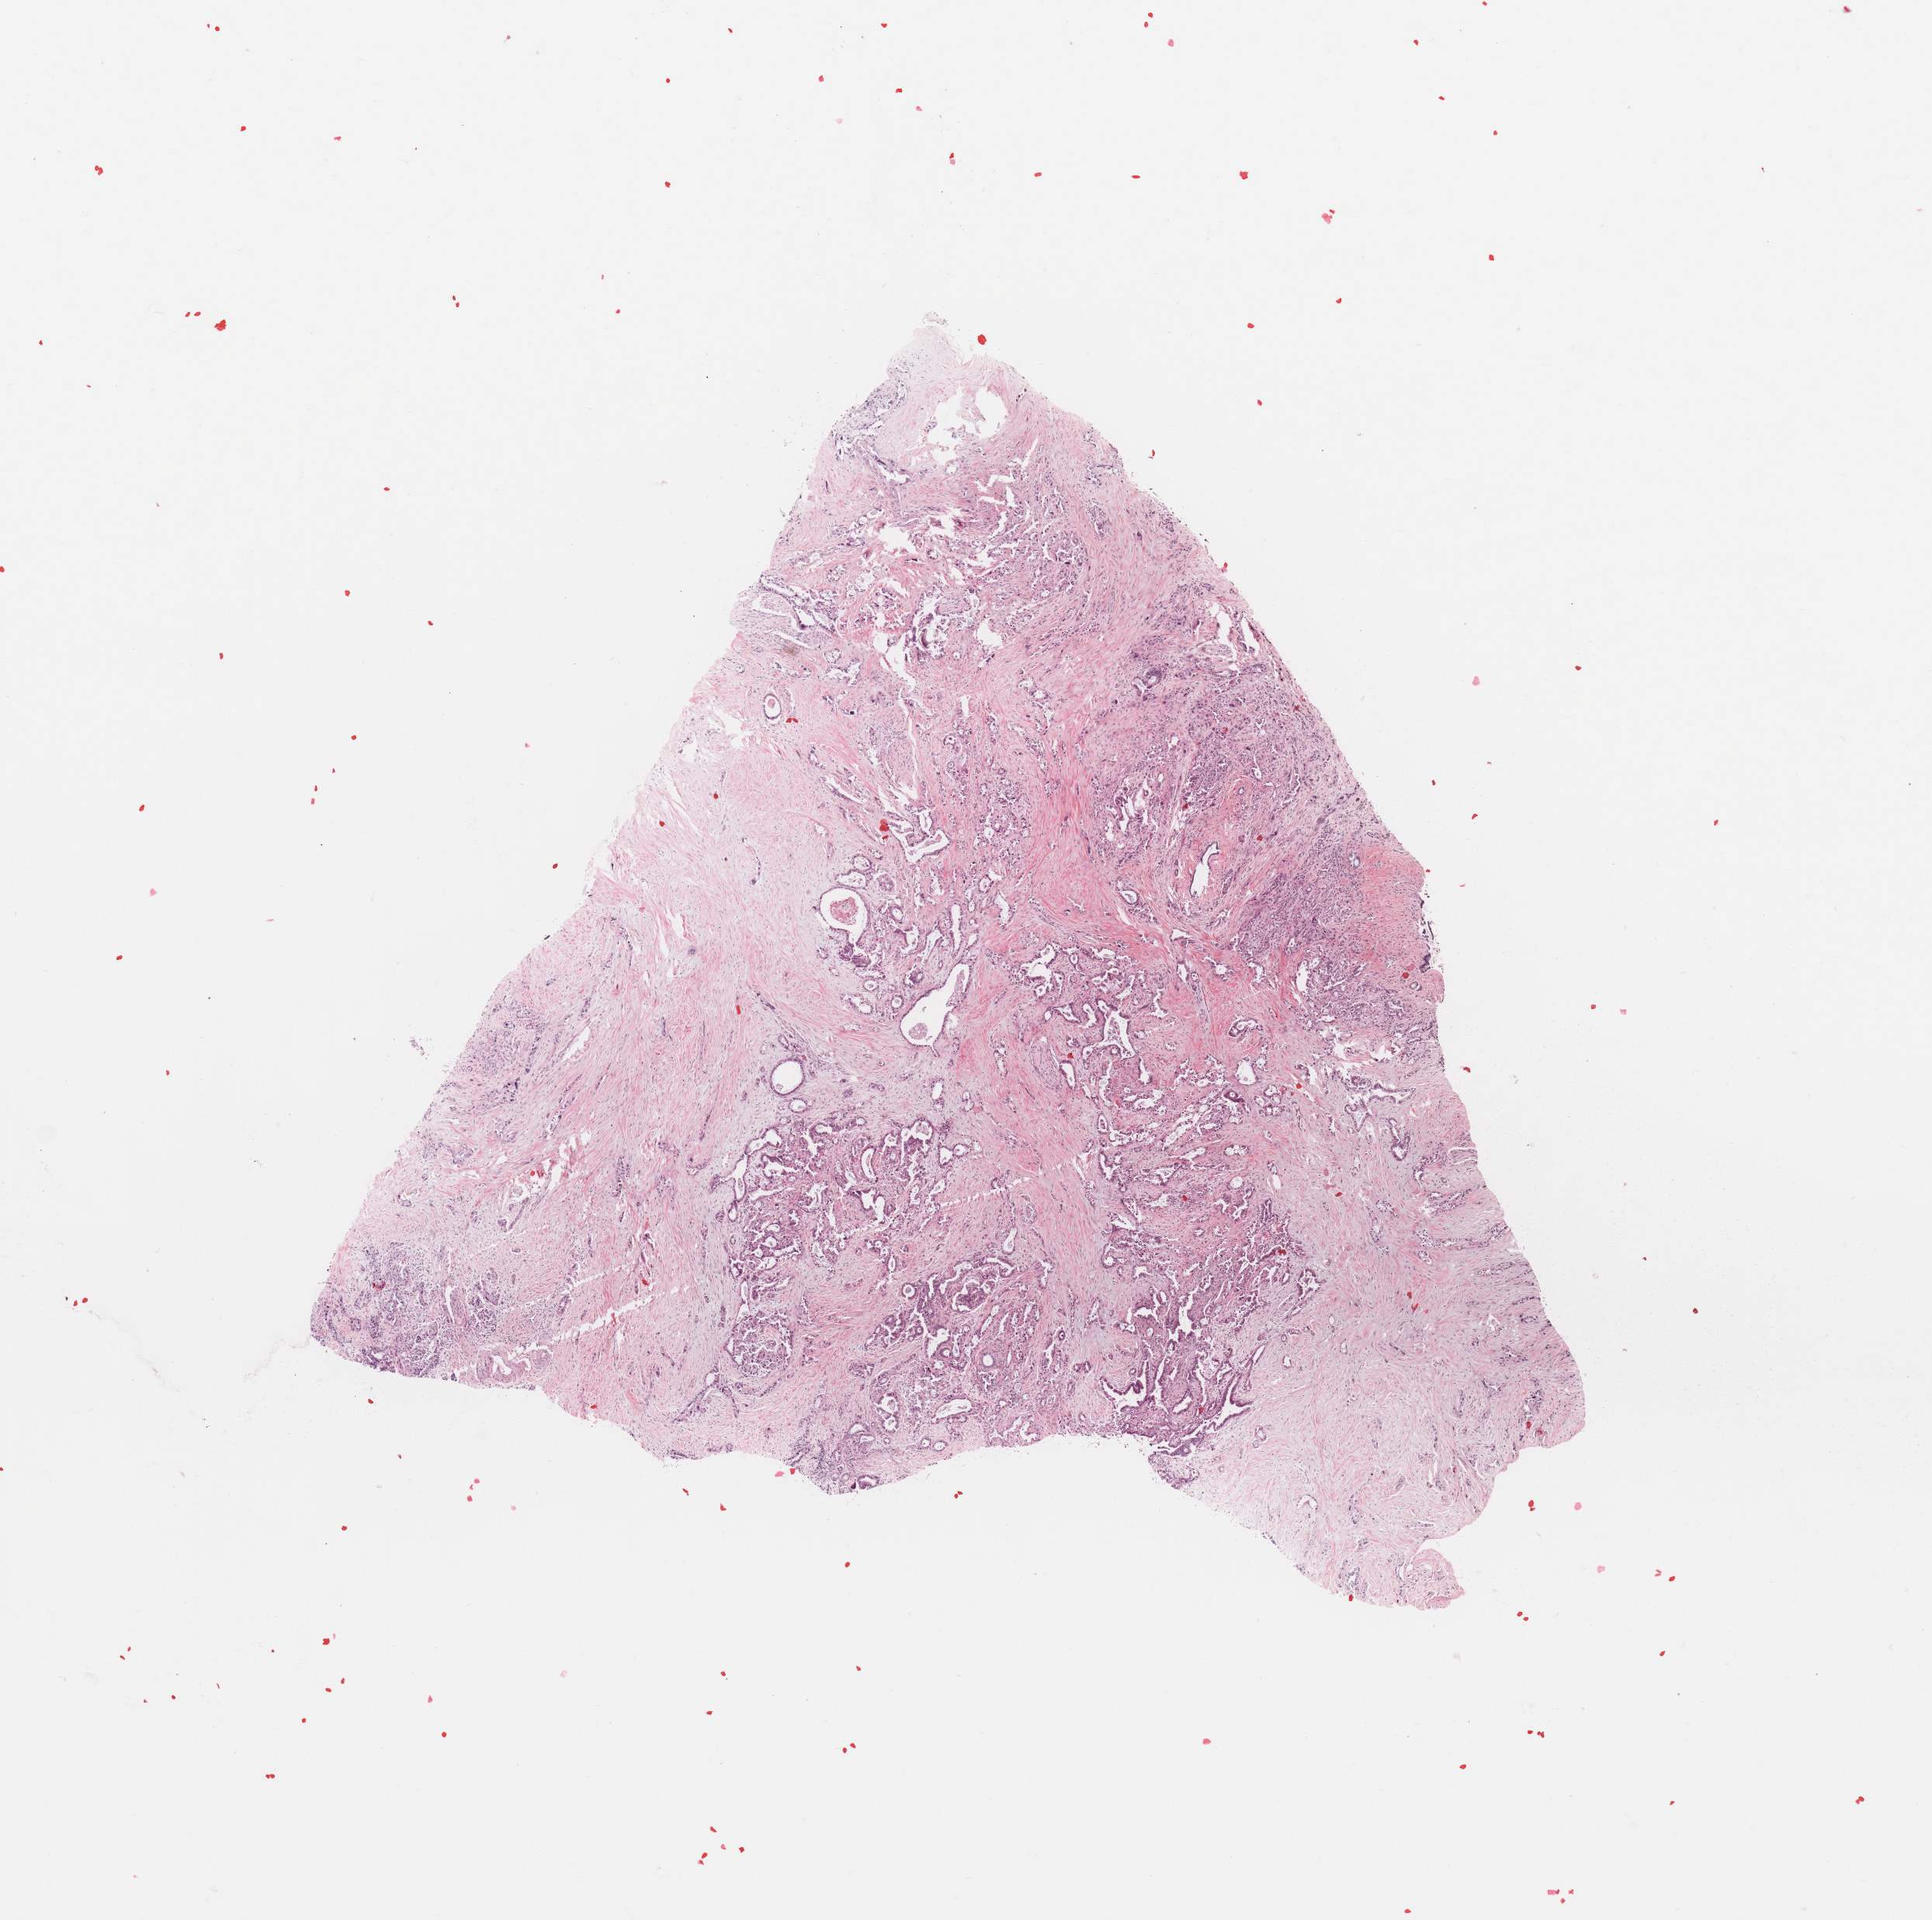
Digitized Hematoxylin and eosin (H&E) stained tissue section (whole slide), whole scanned area (about 9.8 x 9.8 mm) shown as a low-resolution overview; tumour tissue sample, sampled site: pancreas. Patient: female, age 49 years. Histologic grade: G2 (moderately differentiated). Slide review estimates, as recorded: tumour nuclei 30%, necrosis 0%.
• histologic diagnosis: Infiltrating duct carcinoma, NOS
• primary tumour site (as recorded): head
• AJCC pathologic stage: III